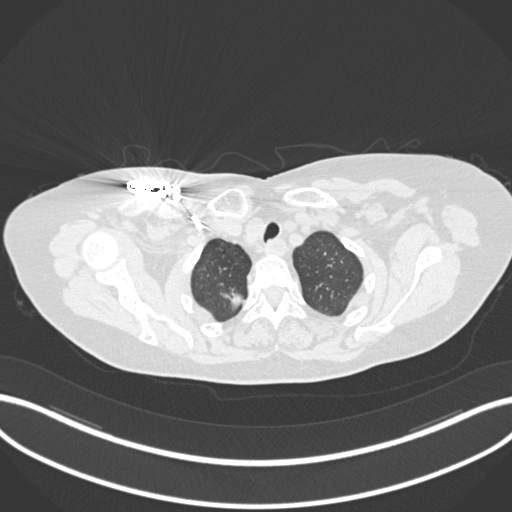
Chest CT, one axial slice. Slice 160 of 176 in the series (ordered by position). Reconstruction kernel B30f. 120 kVp. Lung window (W 1500 / L -600 HU). 1 mm slice thickness. 512 × 512 image matrix, field of view 400 × 400 mm. Patient: female, 72 years. Case-level facts recorded for this patient, not image findings: clinical TNM (as recorded): T1c N0 M0.
Structures marked on this image (rectangle marked by the reading radiologist):
- lung tumour (recorded histology: adenocarcinoma): bounding box <221,289,247,310> (left, top, right, bottom; pixels)